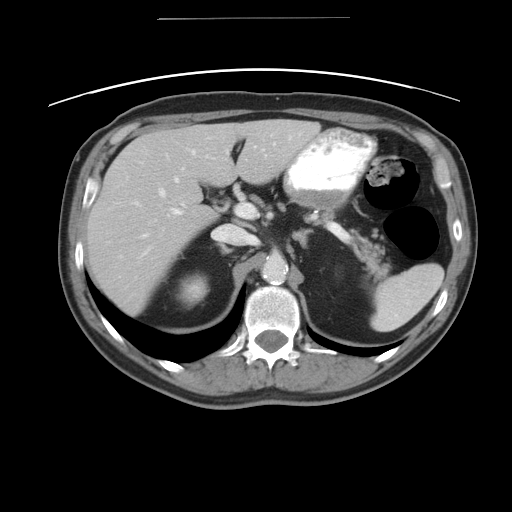
Contrast-enhanced abdominal CT, one axial slice. Slice 28 of 49 in the series (ordered by position). 120 kVp. Soft-tissue window (W 400 / L 40 HU). 5 mm slice thickness. 512 × 512 image matrix, field of view 413 × 413 mm. Male patient, age 57 years. From the clinical record (not read from this slice): diagnosis: colorectal cancer liver metastases, imaged before liver resection; multiple liver metastases: yes; largest metastasis: 4 cm.
Structures marked on this image (manually delineated by an expert):
- hepatic veins: box from (x=119, y=150) to (x=194, y=256) px
- liver: (x=87, y=119)–(x=319, y=314)
- planned liver remnant (the part of the liver to remain after resection): (x=211, y=120)–(x=320, y=187)
- portal vein (with intrahepatic branches): (x=140, y=150)–(x=249, y=255)